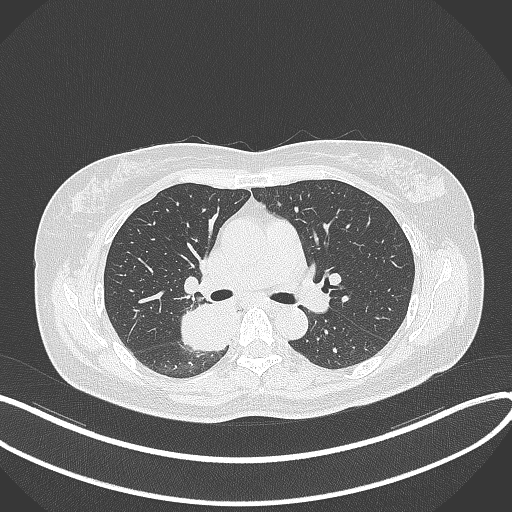
Chest CT, one axial slice. Position 221 of 331 along the scan axis. Lung window (W 1500 / L -600 HU). 512 × 512 image matrix. Female patient, age 54 years. From the clinical record (not read from this slice): clinical TNM (as recorded): T4 N0 M0.
Annotated regions visible in this slice (bounding box drawn by a radiologist):
- lung tumour (recorded histology: adenocarcinoma): box from (x=181, y=298) to (x=237, y=353) px